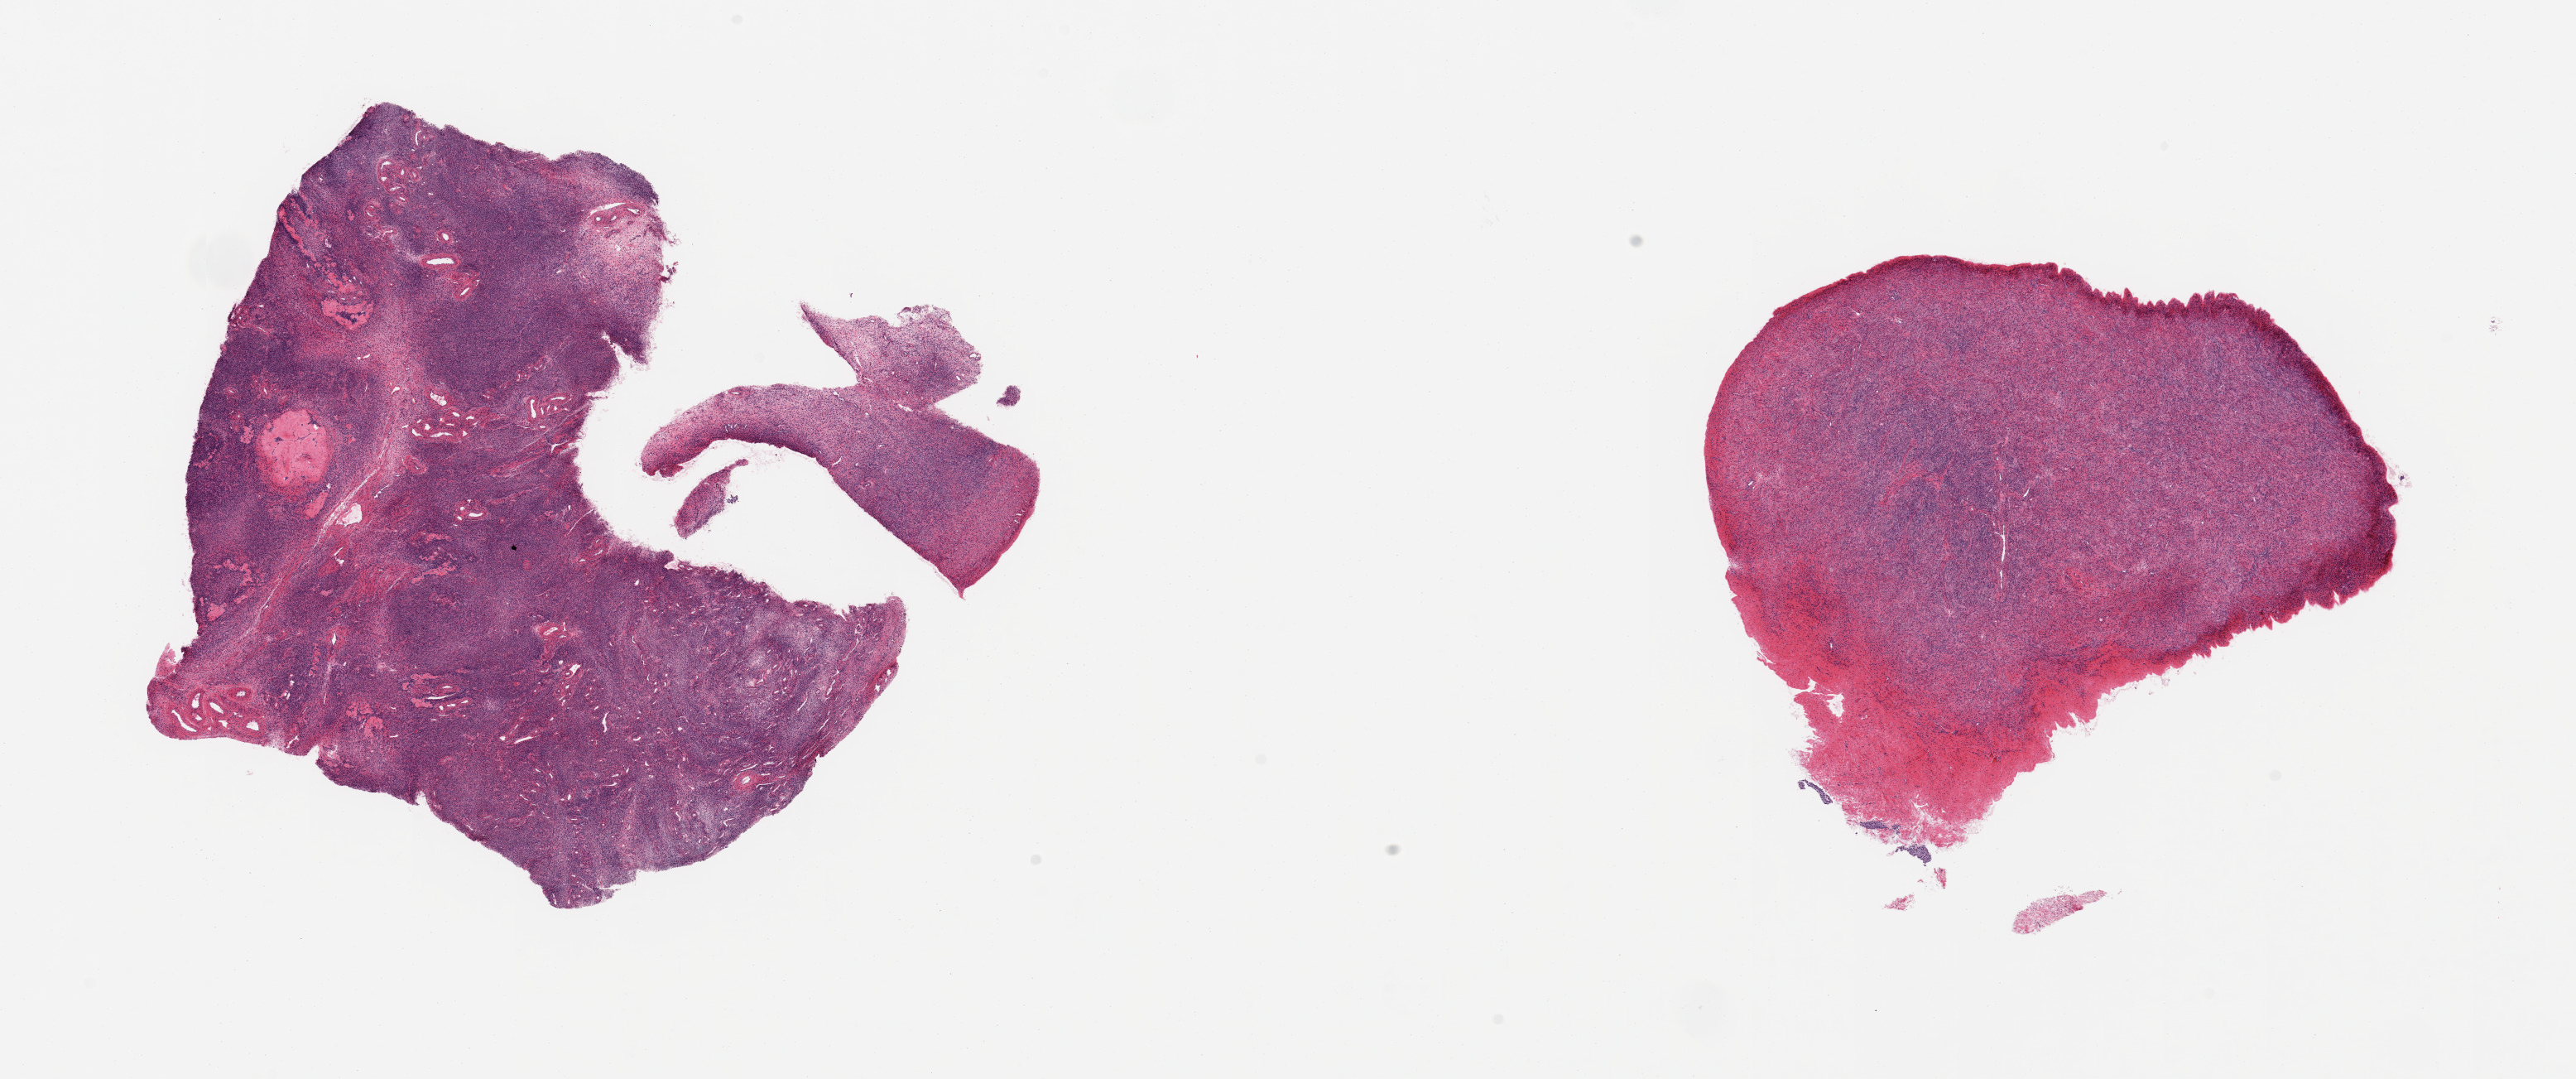
Whole-slide image, hematoxylin and eosin (H&E) stain, brightfield — low-resolution overview of the scanned area, about 24.6 x 10.3 mm (slide scanned at 20x), PAXgene-fixed, paraffin-embedded tissue, section of ovary (target tissue), tissue donor sample.
Review note (as recorded): 2 pieces; corpora albicans & rare ova.